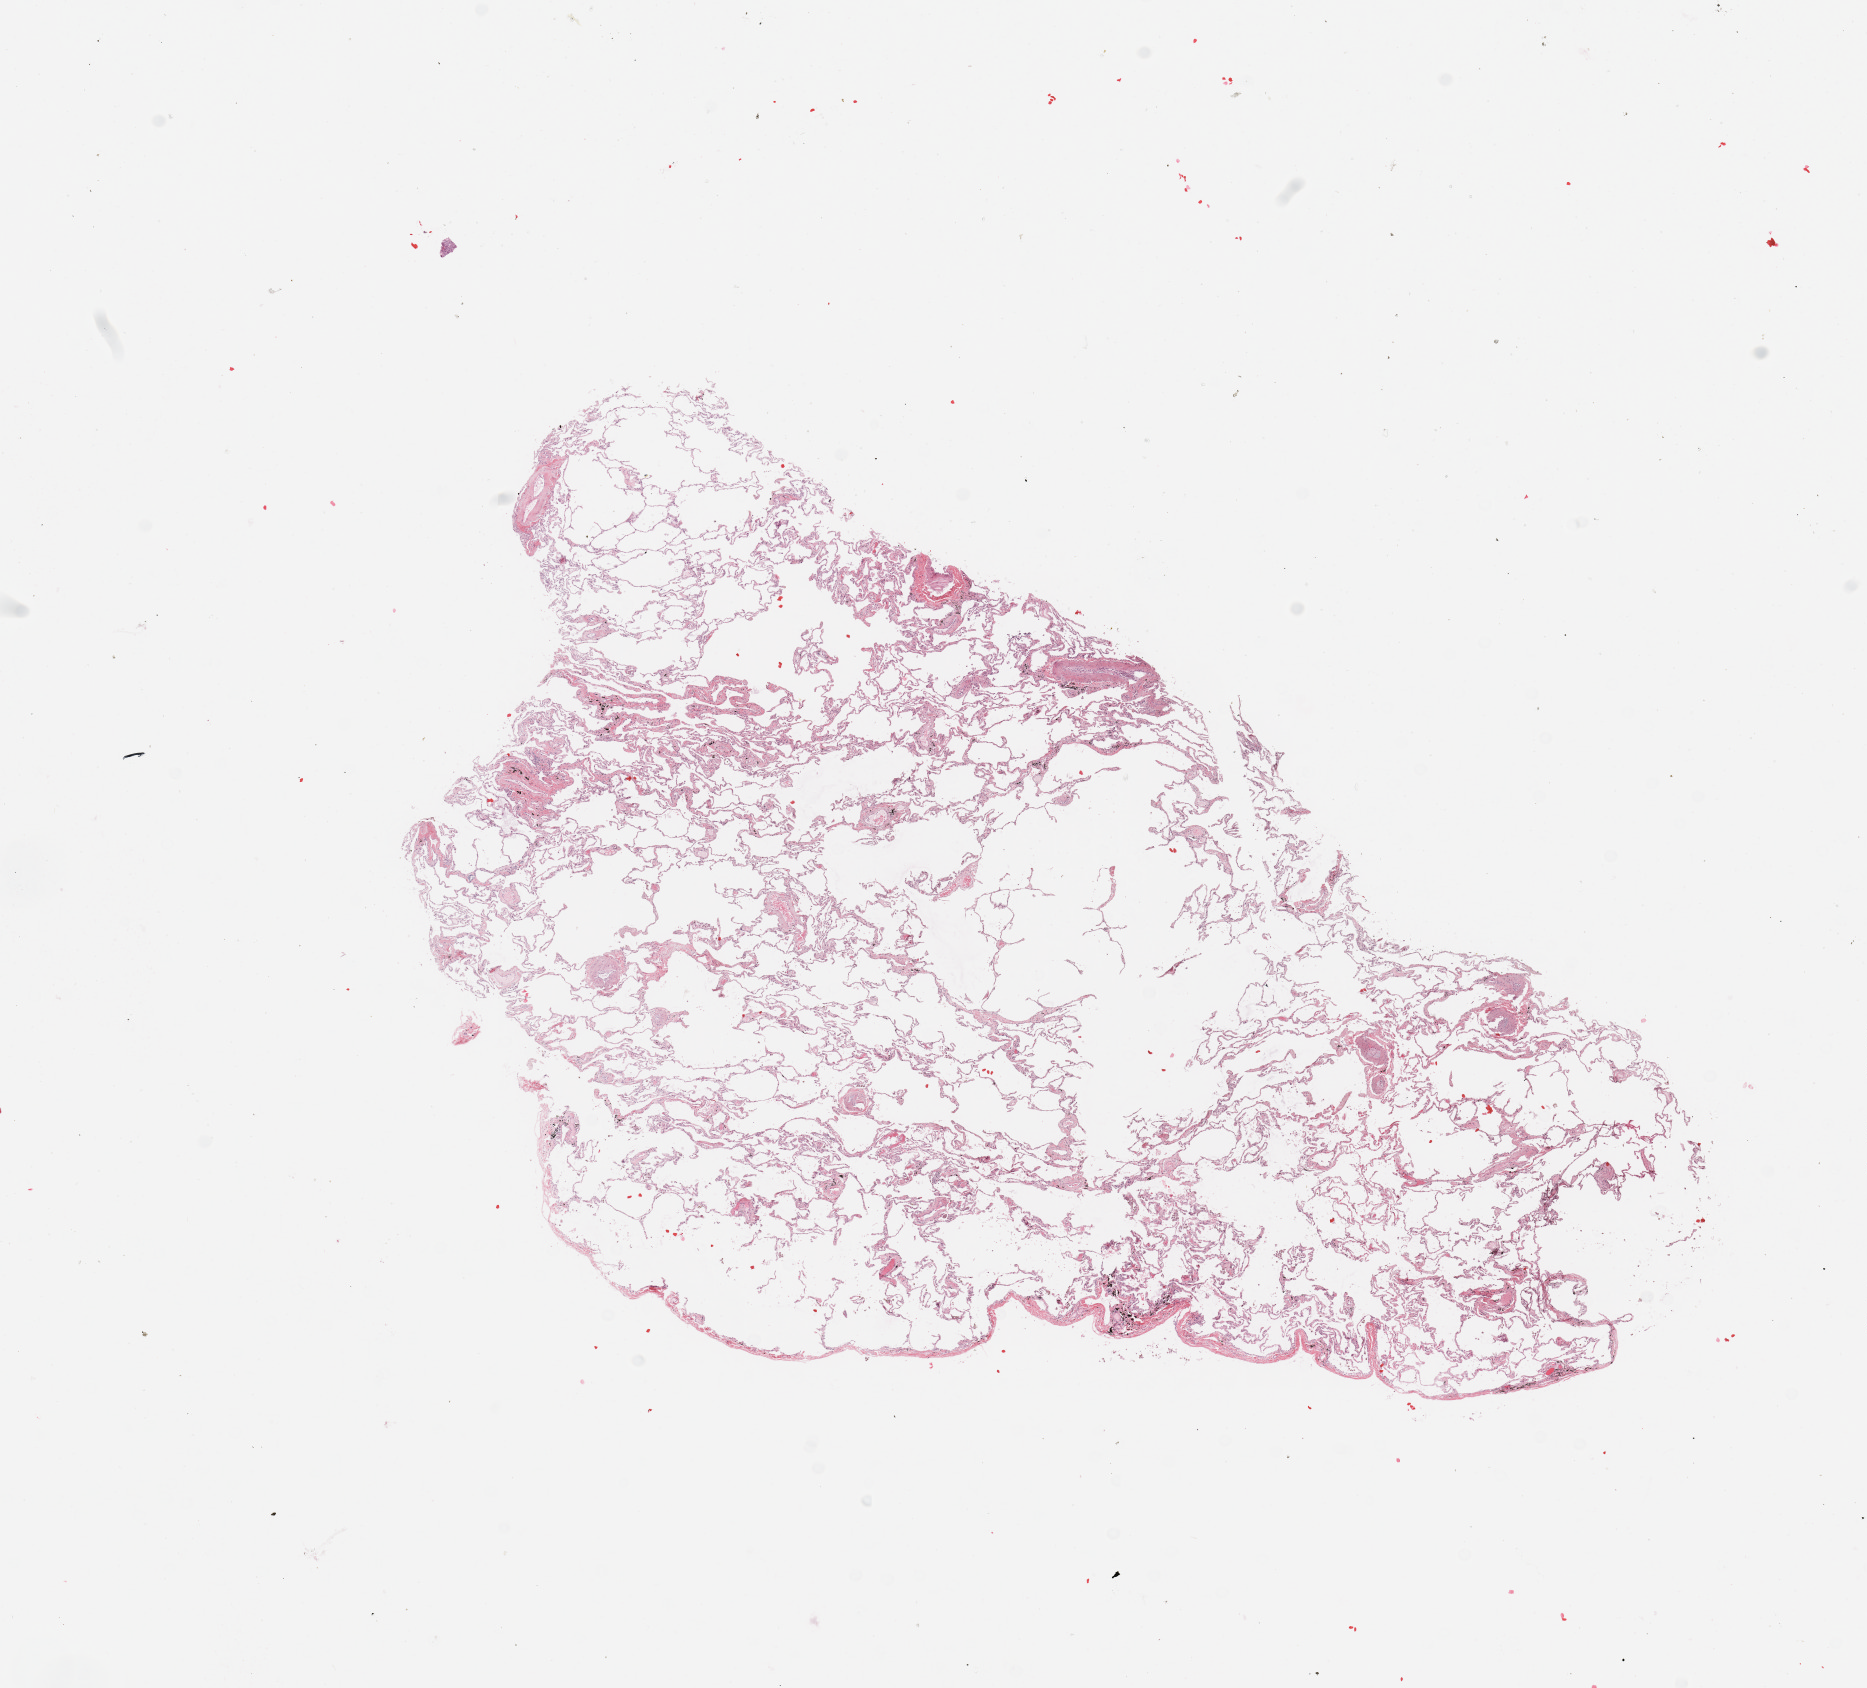
H&E whole-slide image — whole scanned area (about 14.8 x 13.4 mm) shown as a low-resolution overview, normal (non-tumour) tissue sample, sampled site: lung. 76-year-old male patient.
This section: normal (non-tumour) tissue from the same patient. Patient diagnosis: Squamous cell carcinoma, NOS.